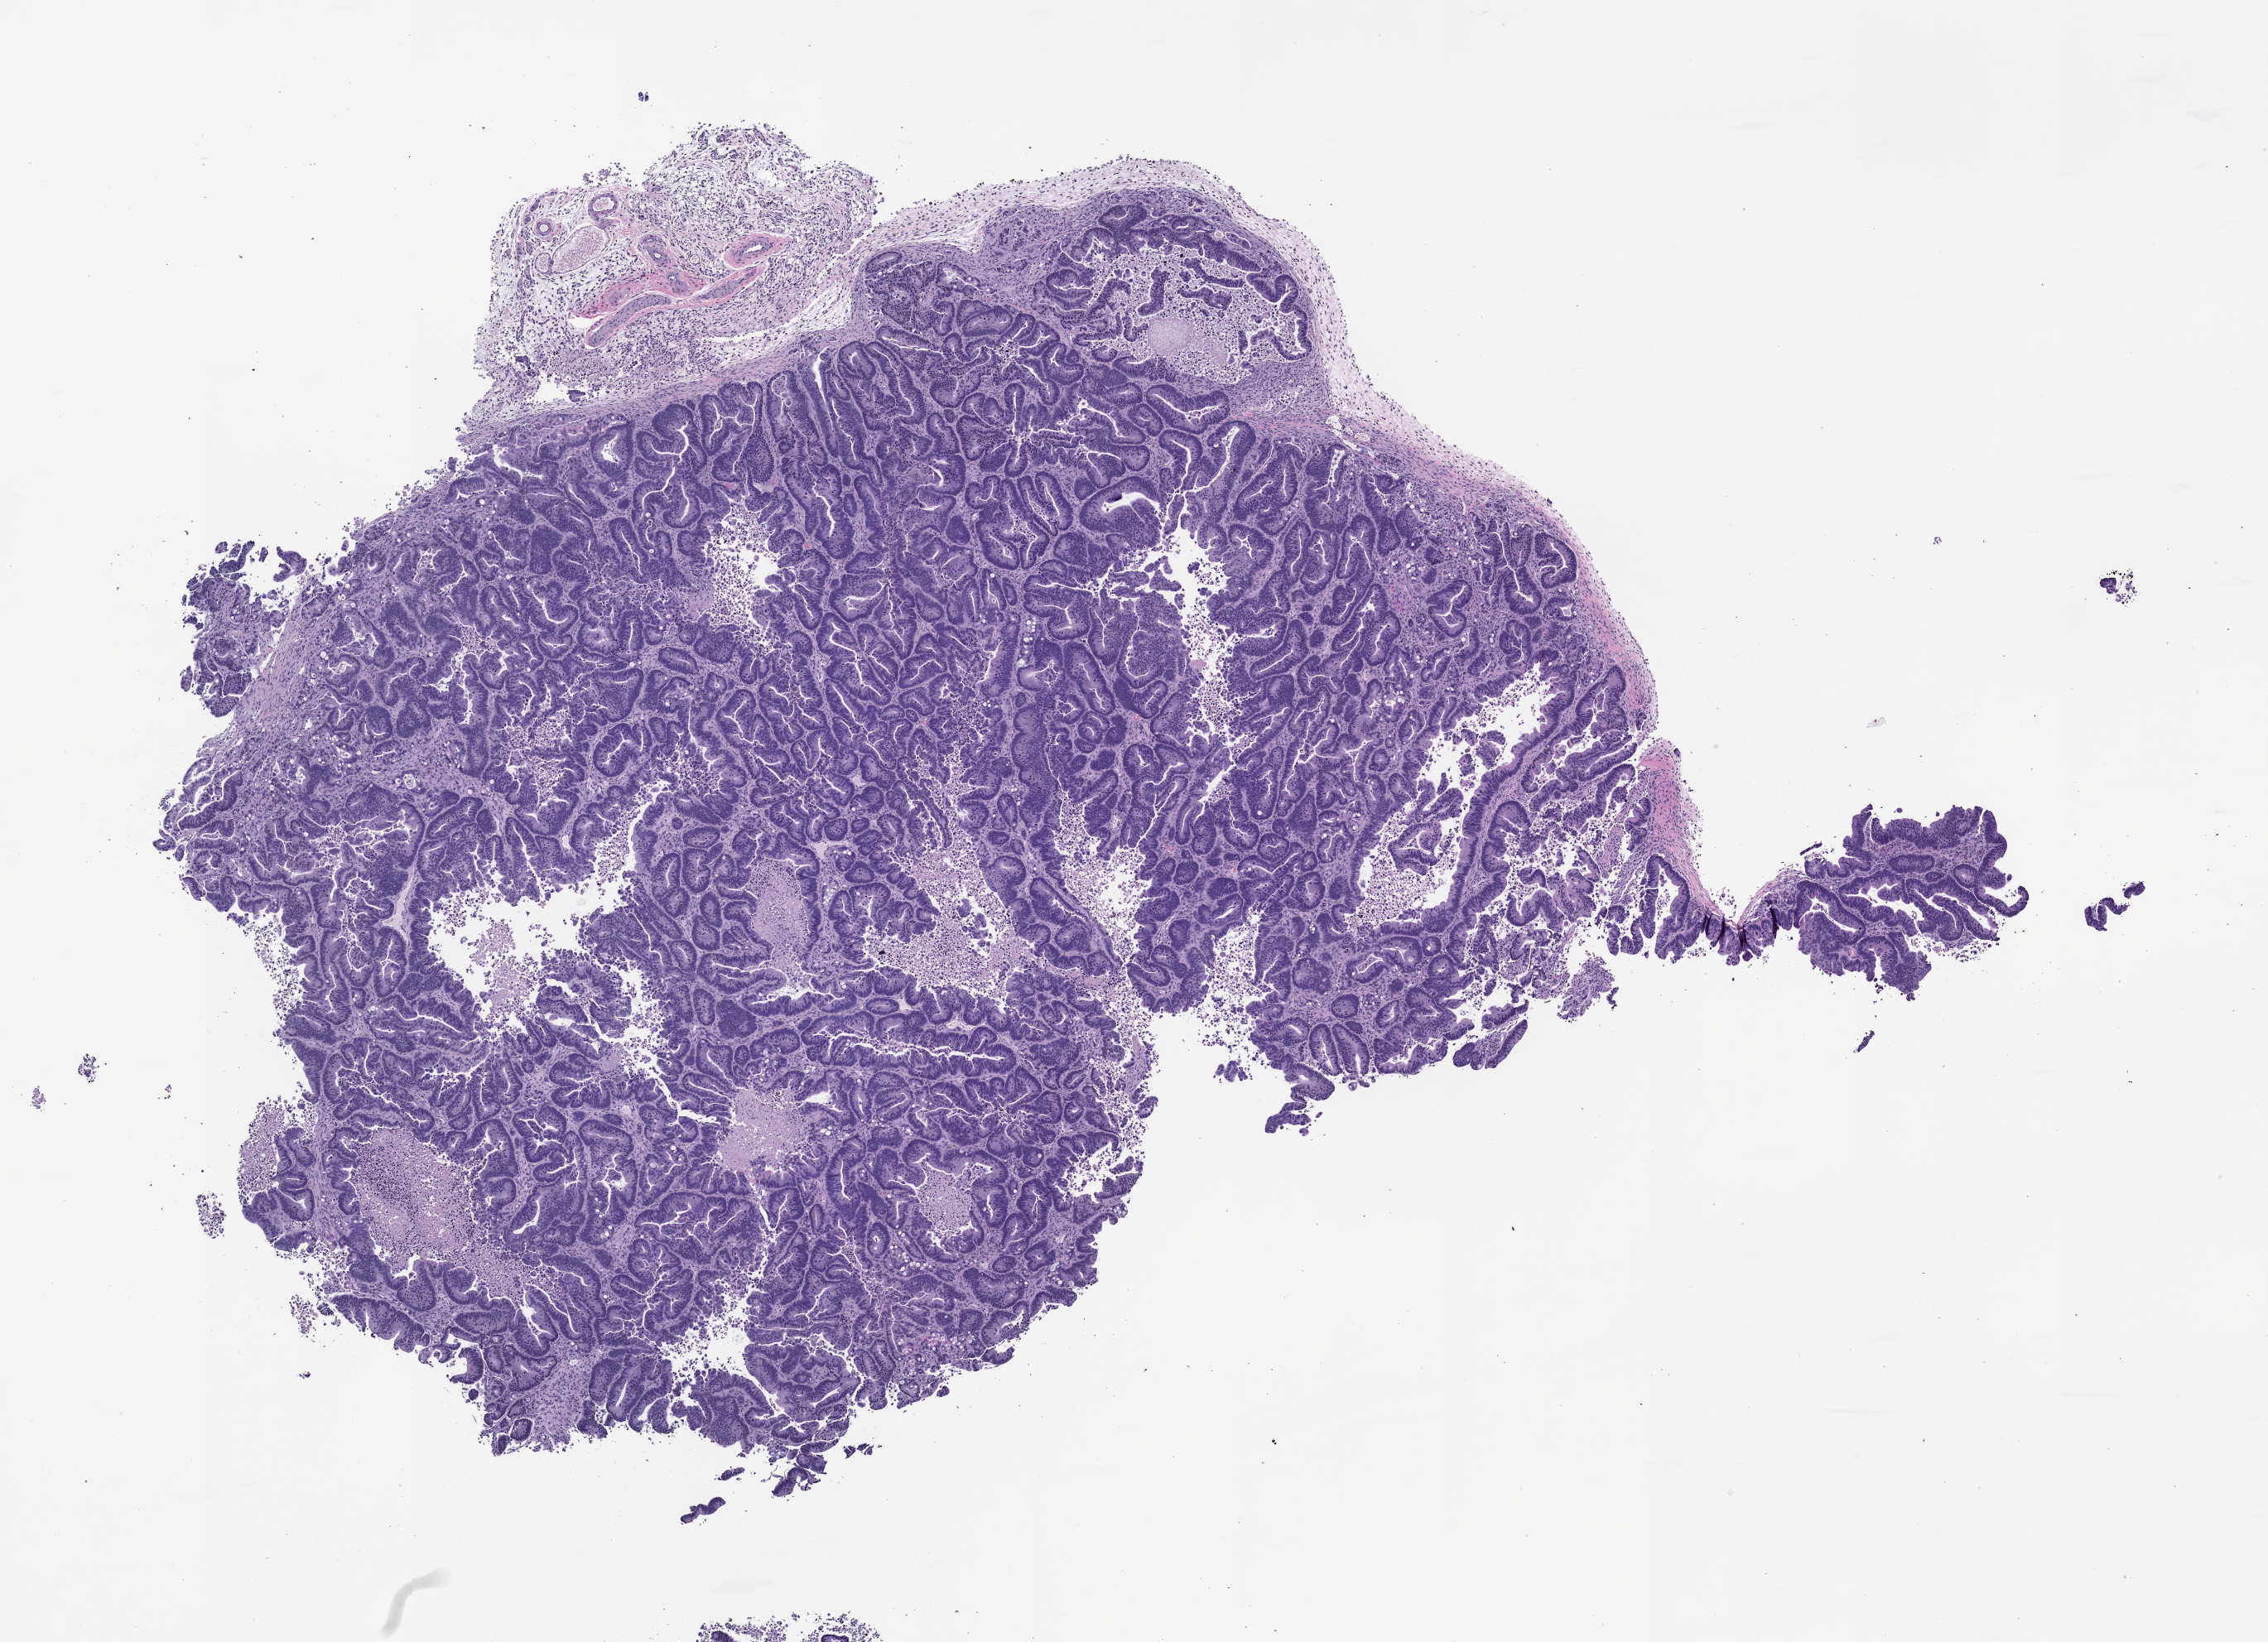
H&E whole-slide image of a patient-derived xenograft (PDX) tumor grown in a mouse, passage 2, shown as a low-resolution overview of the whole scanned area (about 11.0 x 8.0 mm), formalin-fixed, paraffin-embedded (FFPE) tissue, originating tumor site category: gastrointestinal tract.
Originating patient diagnosis: Colorectal Carcinoma.